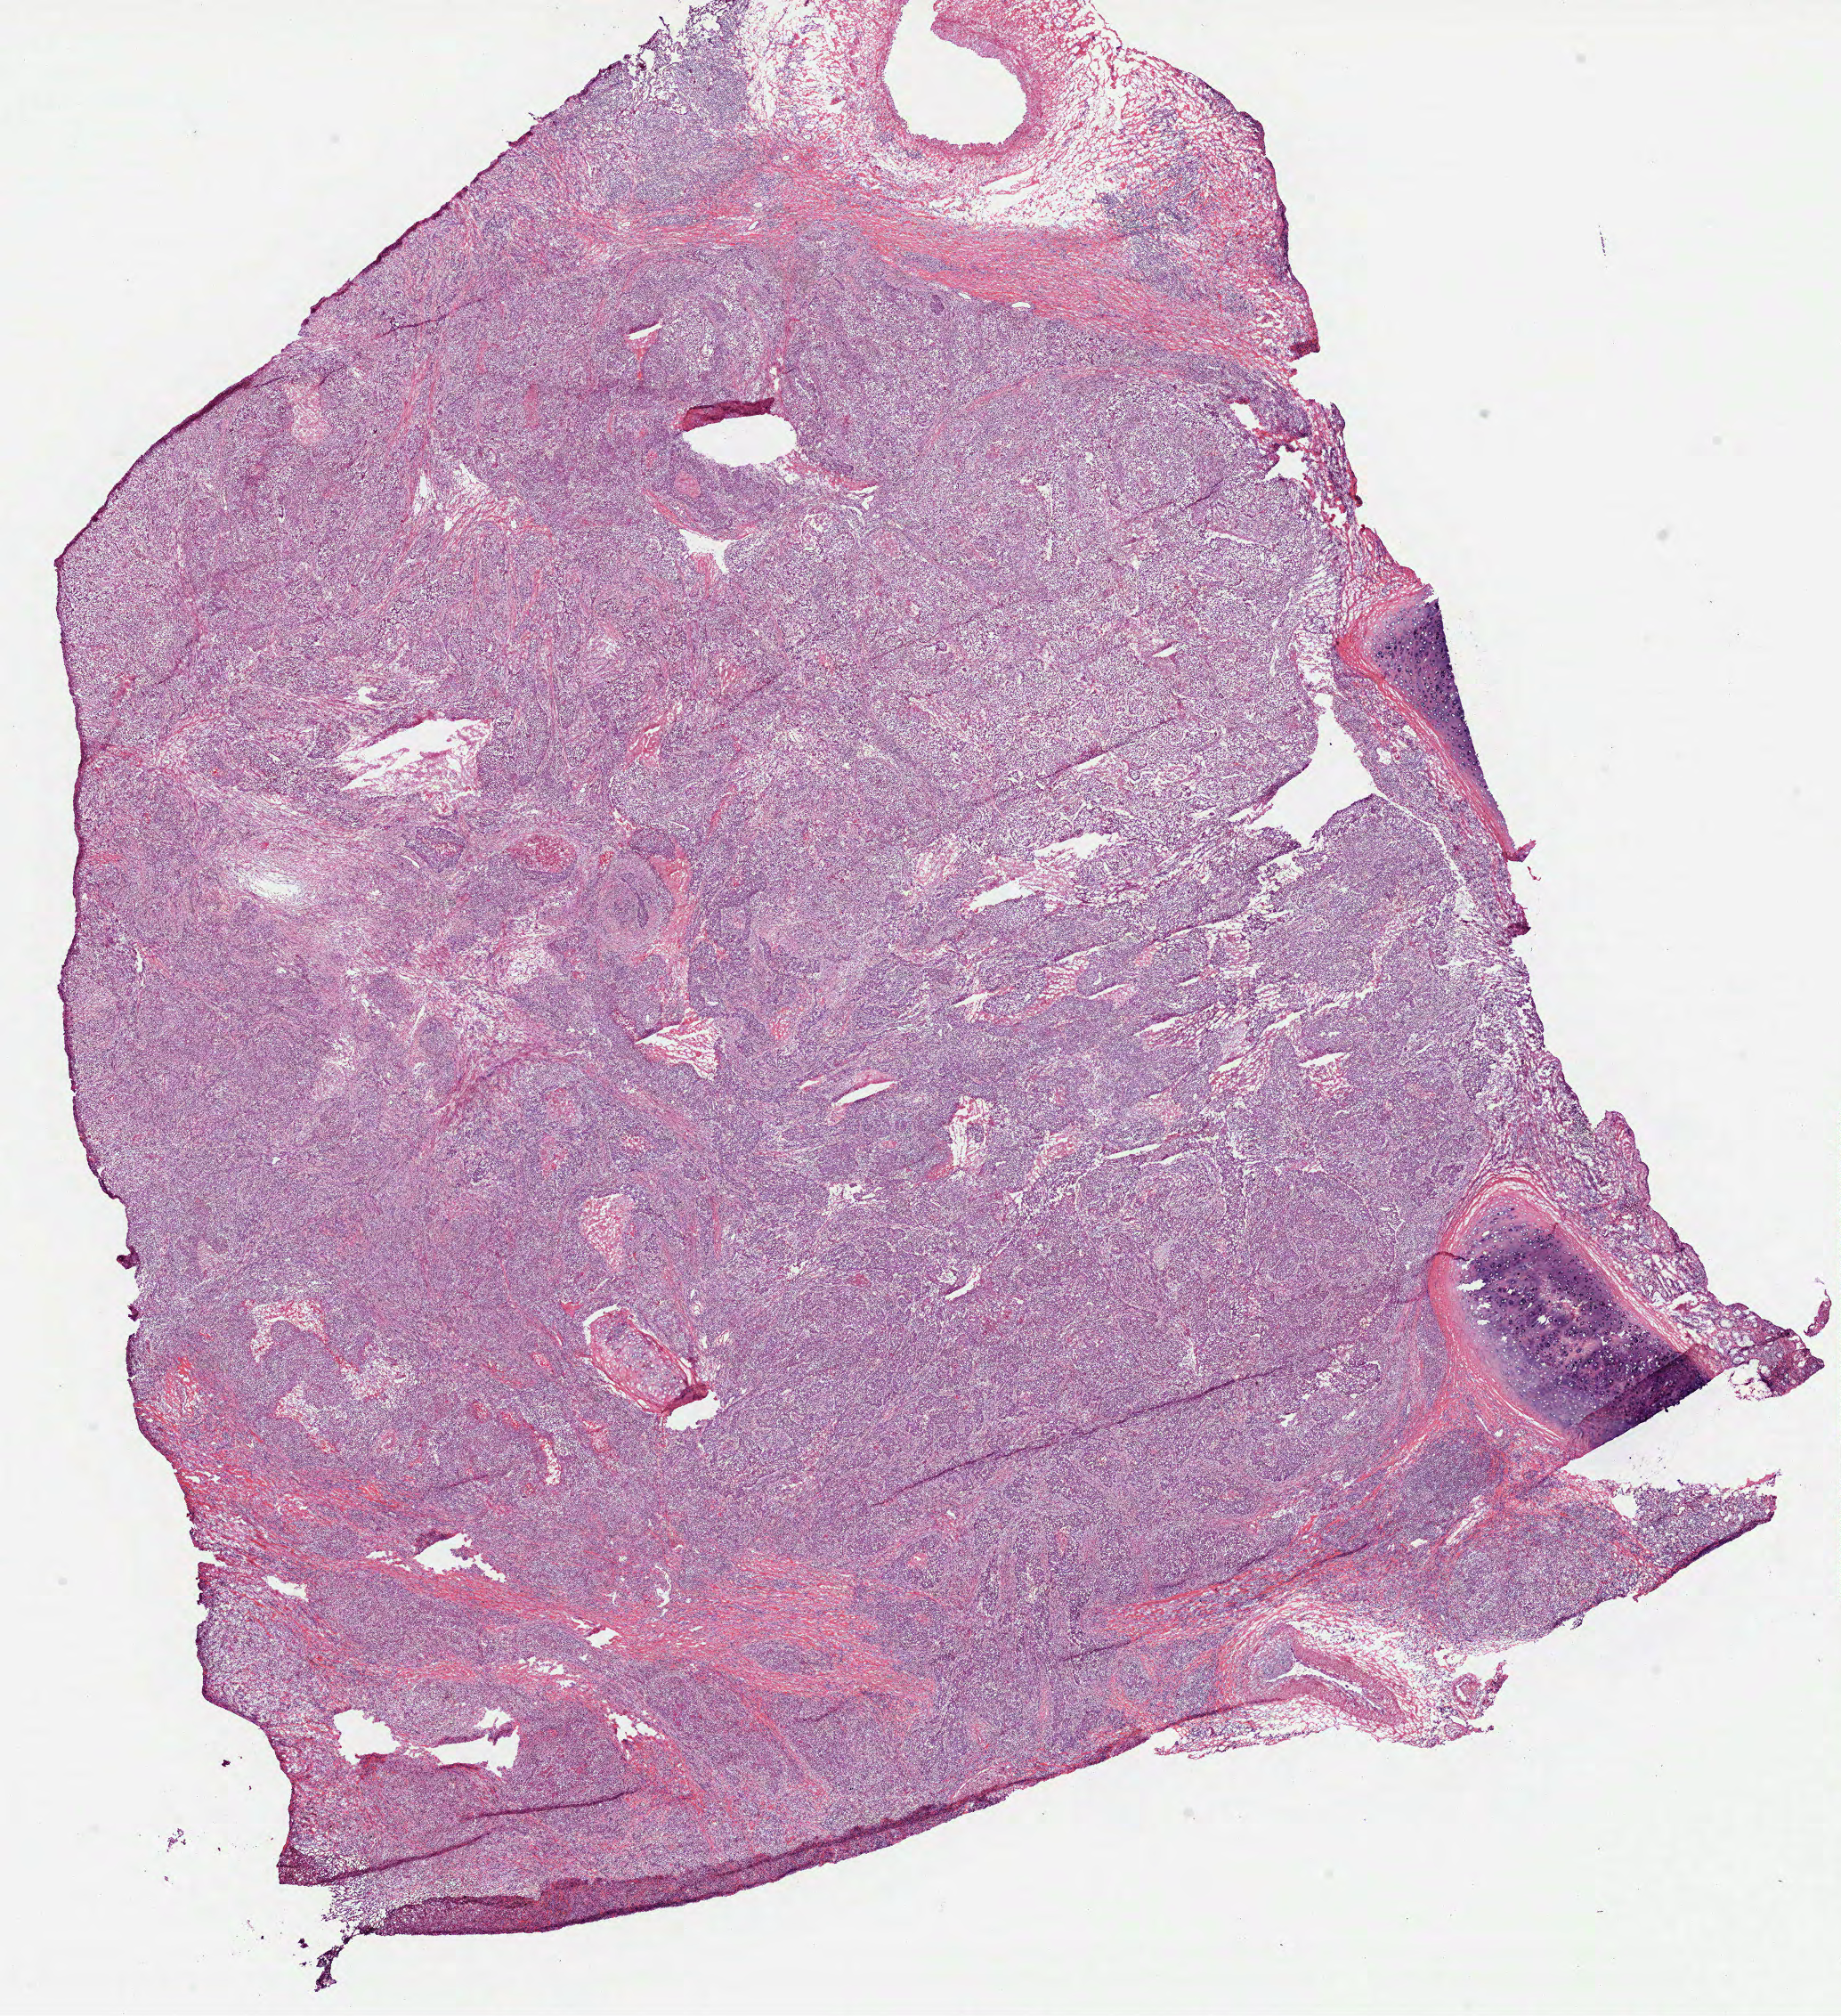
Digitized H&E tissue section (whole slide), whole scanned area (about 16.7 x 18.3 mm) shown as a low-resolution overview, frozen section, sample: primary tumour, lung. Male, age 73 years at initial diagnosis. Pathologist review of this section (percent, as recorded): tumour cells 80%, tumour nuclei 75%, normal cells 2%, stromal cells 11%, necrosis 7%. Inflammatory infiltration, as recorded: lymphocyte infiltration 10%.
- pathologic diagnosis: Squamous cell carcinoma, NOS
- AJCC pathologic stage: IIIA